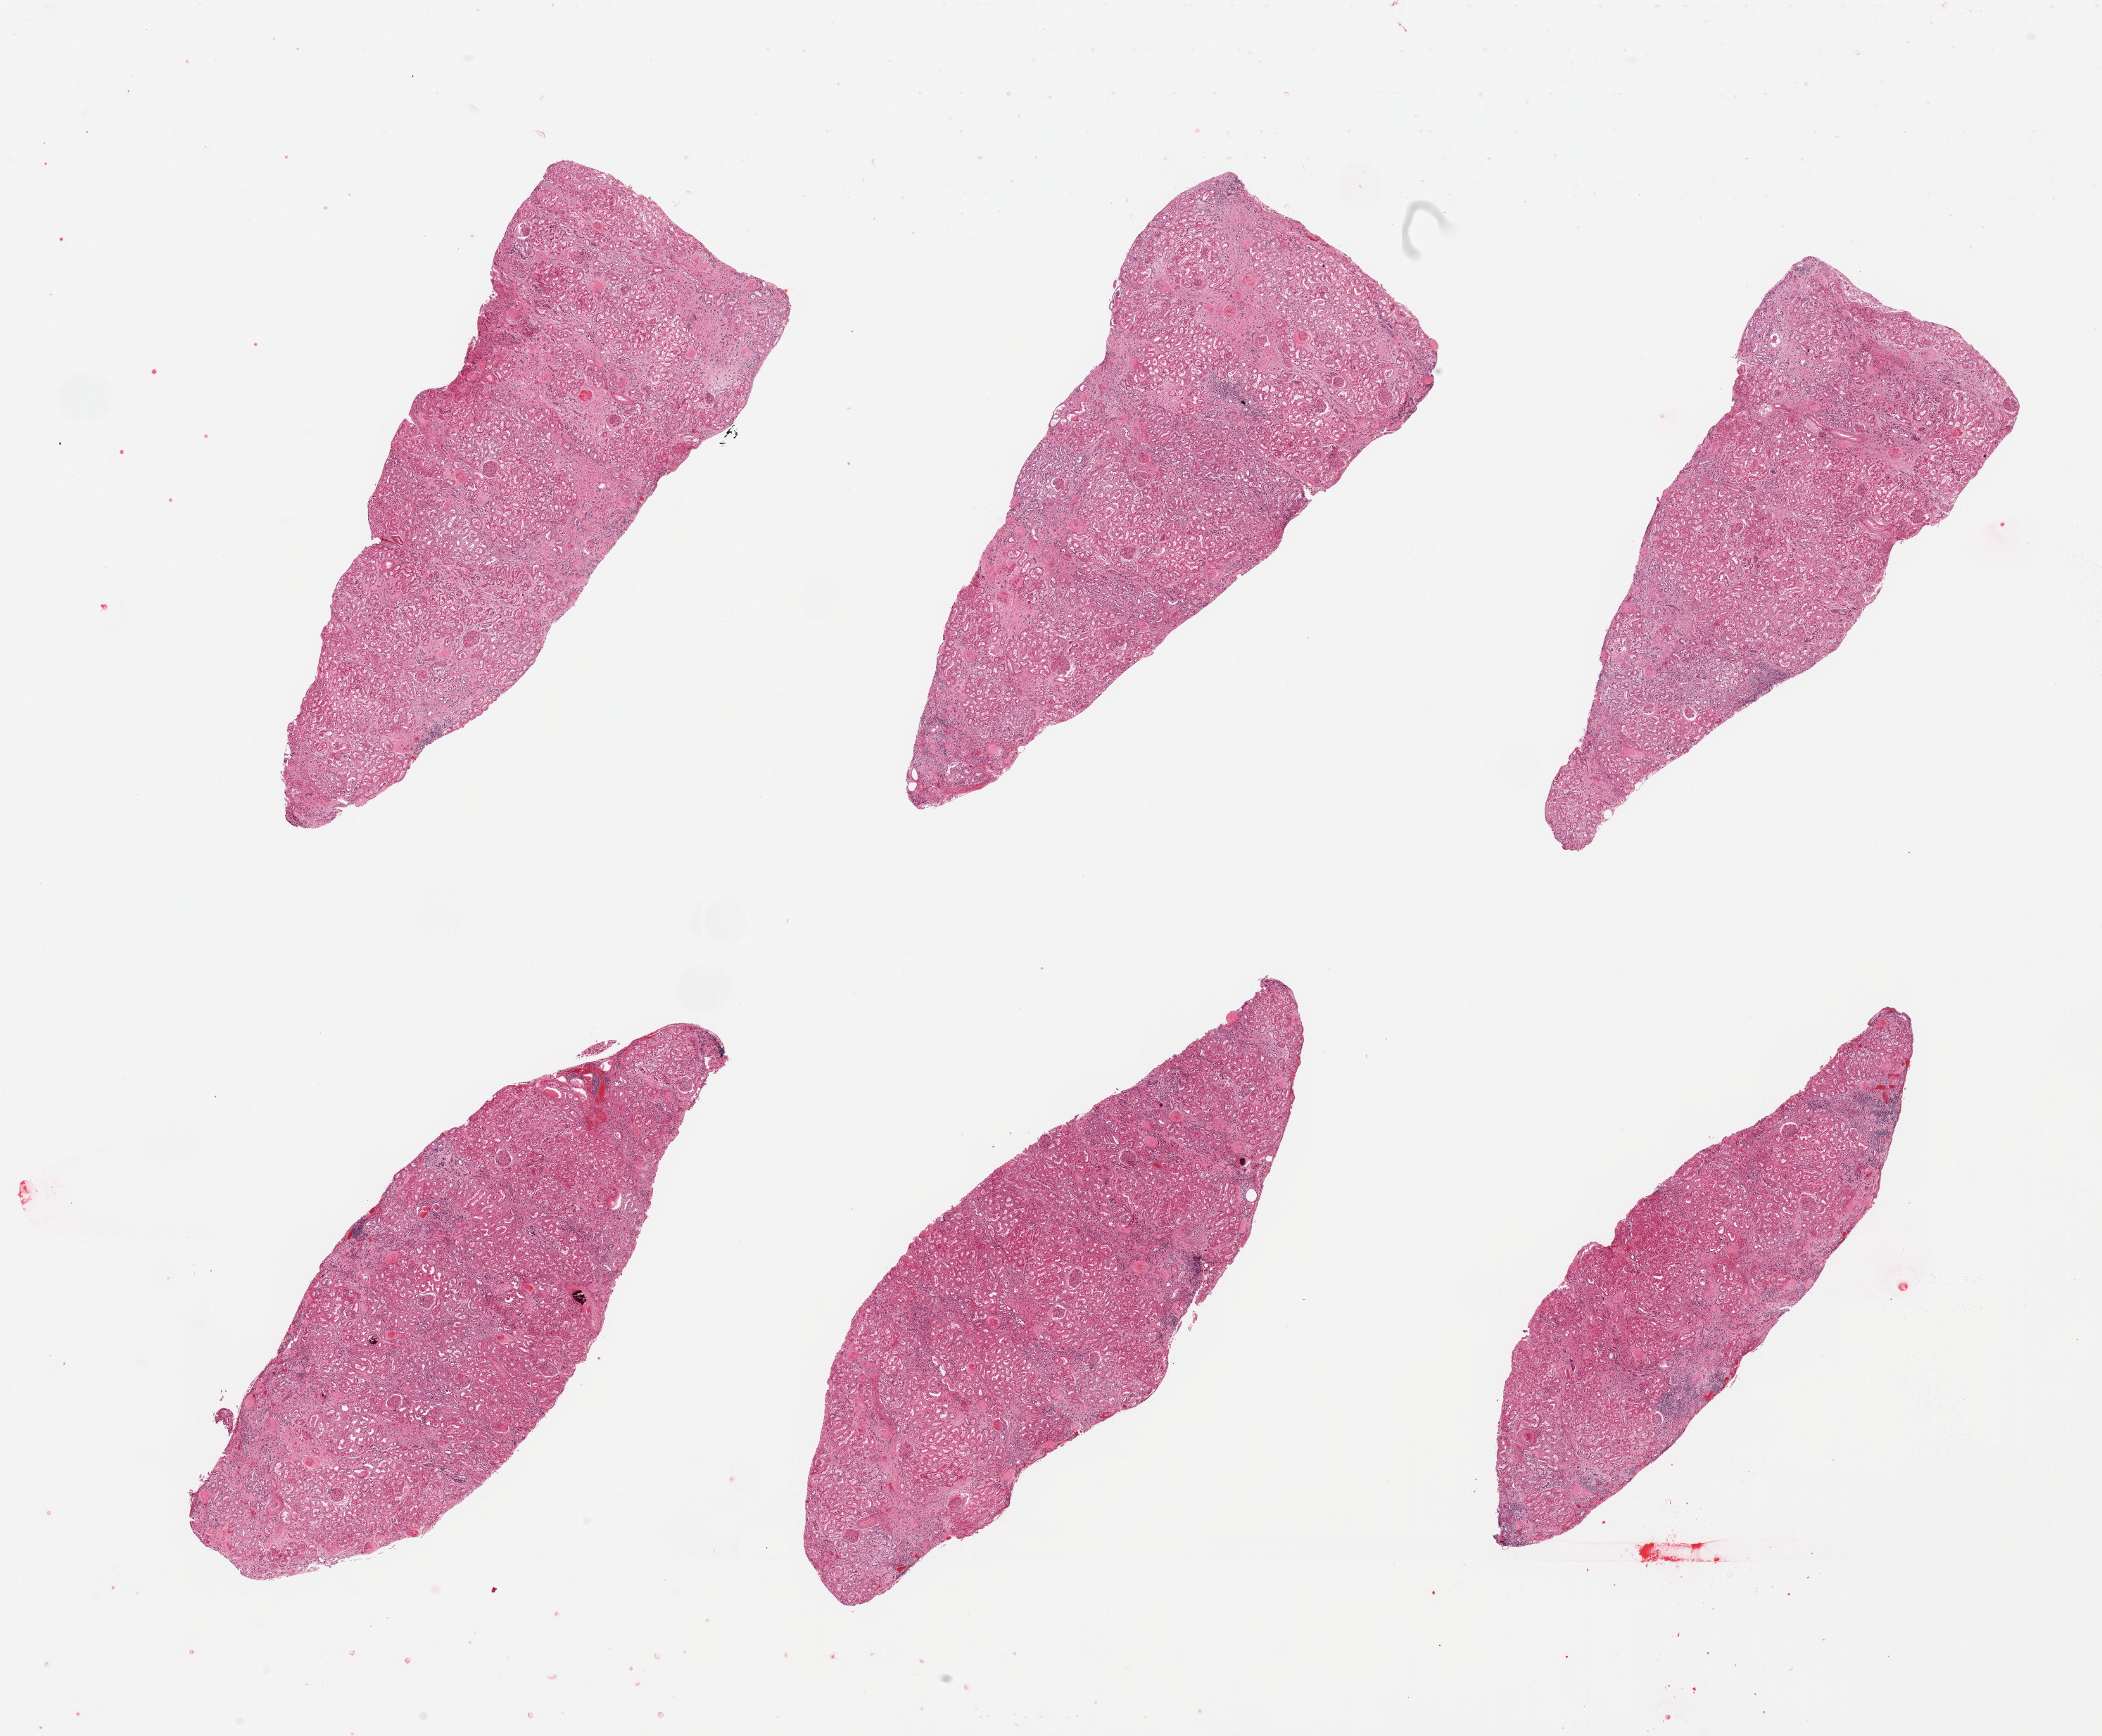
Haematoxylin and eosin whole-slide image — shown as a low-resolution overview of the whole scanned area (about 23.6 x 19.5 mm, from a 20x scan); PAXgene-fixed, paraffin-embedded tissue; target tissue: renal cortex; donor tissue sample. Donor: female.
Reviewer comment on this tissue sample: 6 pieces; diffuse and nodular glomerulosclerosis, vascular thickening, interstitial fibrosis and chronic inflammation.